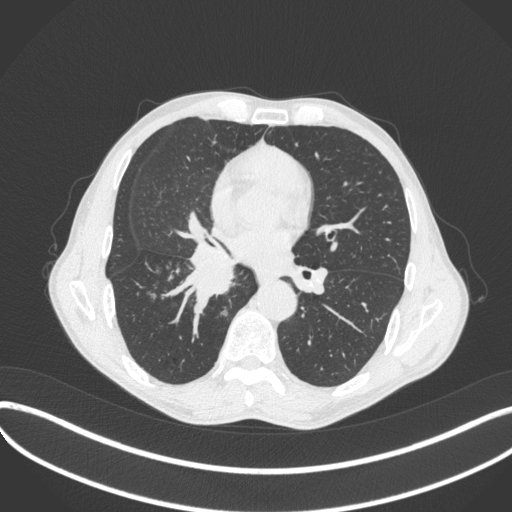
Chest CT, one axial slice. Reconstruction kernel B31f. 120 kVp. Lung window (W 1500 / L -600 HU). 1 mm slice thickness. 512 × 512 image matrix, field of view 400 × 400 mm. Male patient, age 65 years. Case-level facts recorded for this patient, not image findings: clinical TNM (as recorded): T2a N0 M0; histopathological grade: G2.
Annotated regions visible in this slice (rectangle marked by the reading radiologist):
- lung tumour (recorded histology: squamous cell carcinoma): bounding box [x1, y1, x2, y2] px = [185, 243, 238, 297]